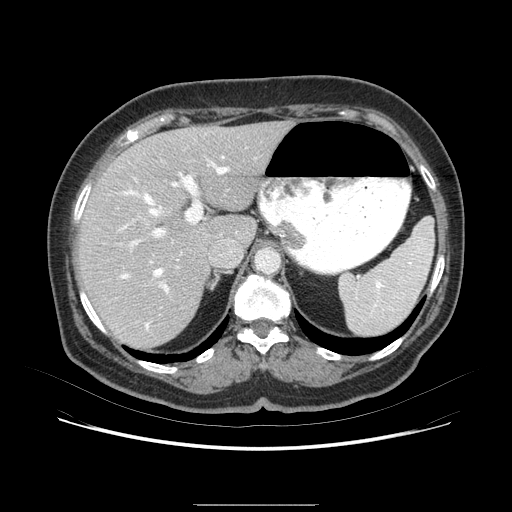
Contrast-enhanced abdominal CT (liver protocol), one axial slice; position 52 of 79 along the scan axis; 120 kVp; soft-tissue window (W 400 / L 40 HU); 512 × 512 image matrix, field of view 380 × 380 mm. Case-level facts recorded for this patient, not image findings: diagnosis: hepatocellular carcinoma (patient treated with transarterial chemoembolisation; whether this scan precedes or follows treatment is not stated here); TNM stage (as recorded): Stage-I; Child-Pugh class: A; tumour nodularity: uninodular.
Structures marked on this image (semi-automatically segmented with operator editing):
- abdominal aorta: bounding box [x1, y1, x2, y2] px = [257, 249, 282, 277]
- liver parenchyma outside the tumour (the mass and vessels are separate outlines, so this box may not span the whole liver): [76, 124, 298, 344]
- liver vessels: [116, 155, 267, 315]